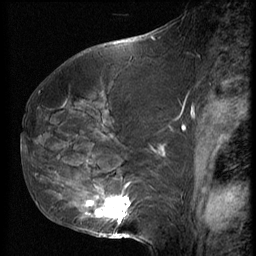
Breast MRI (dynamic contrast-enhanced), one sagittal slice. Position 31 of 62 along the scan axis. 3 images stored at this slice position (order not interpretable as contrast timing). 1.5 T. TE 4.2 ms, TR 9 ms. 2.5 mm slice thickness. 256 × 256 image matrix. Patient: female, 50 years. From the clinical record (not read from this slice): setting: breast cancer imaged before/during neoadjuvant chemotherapy; receptor status: HR-positive, HER2-negative.
Annotated regions visible in this slice (semi-automatically segmented with operator editing):
- analysis volume of interest (the breast-tissue region the enhancement analysis was run in; not a lesion): bounding box (x1, y1, x2, y2) in pixels: (59, 125, 139, 238)
- tumour enhancement mask (voxels above the 140 % enhancement threshold inside the analysis volume of interest): (89, 197, 131, 222)